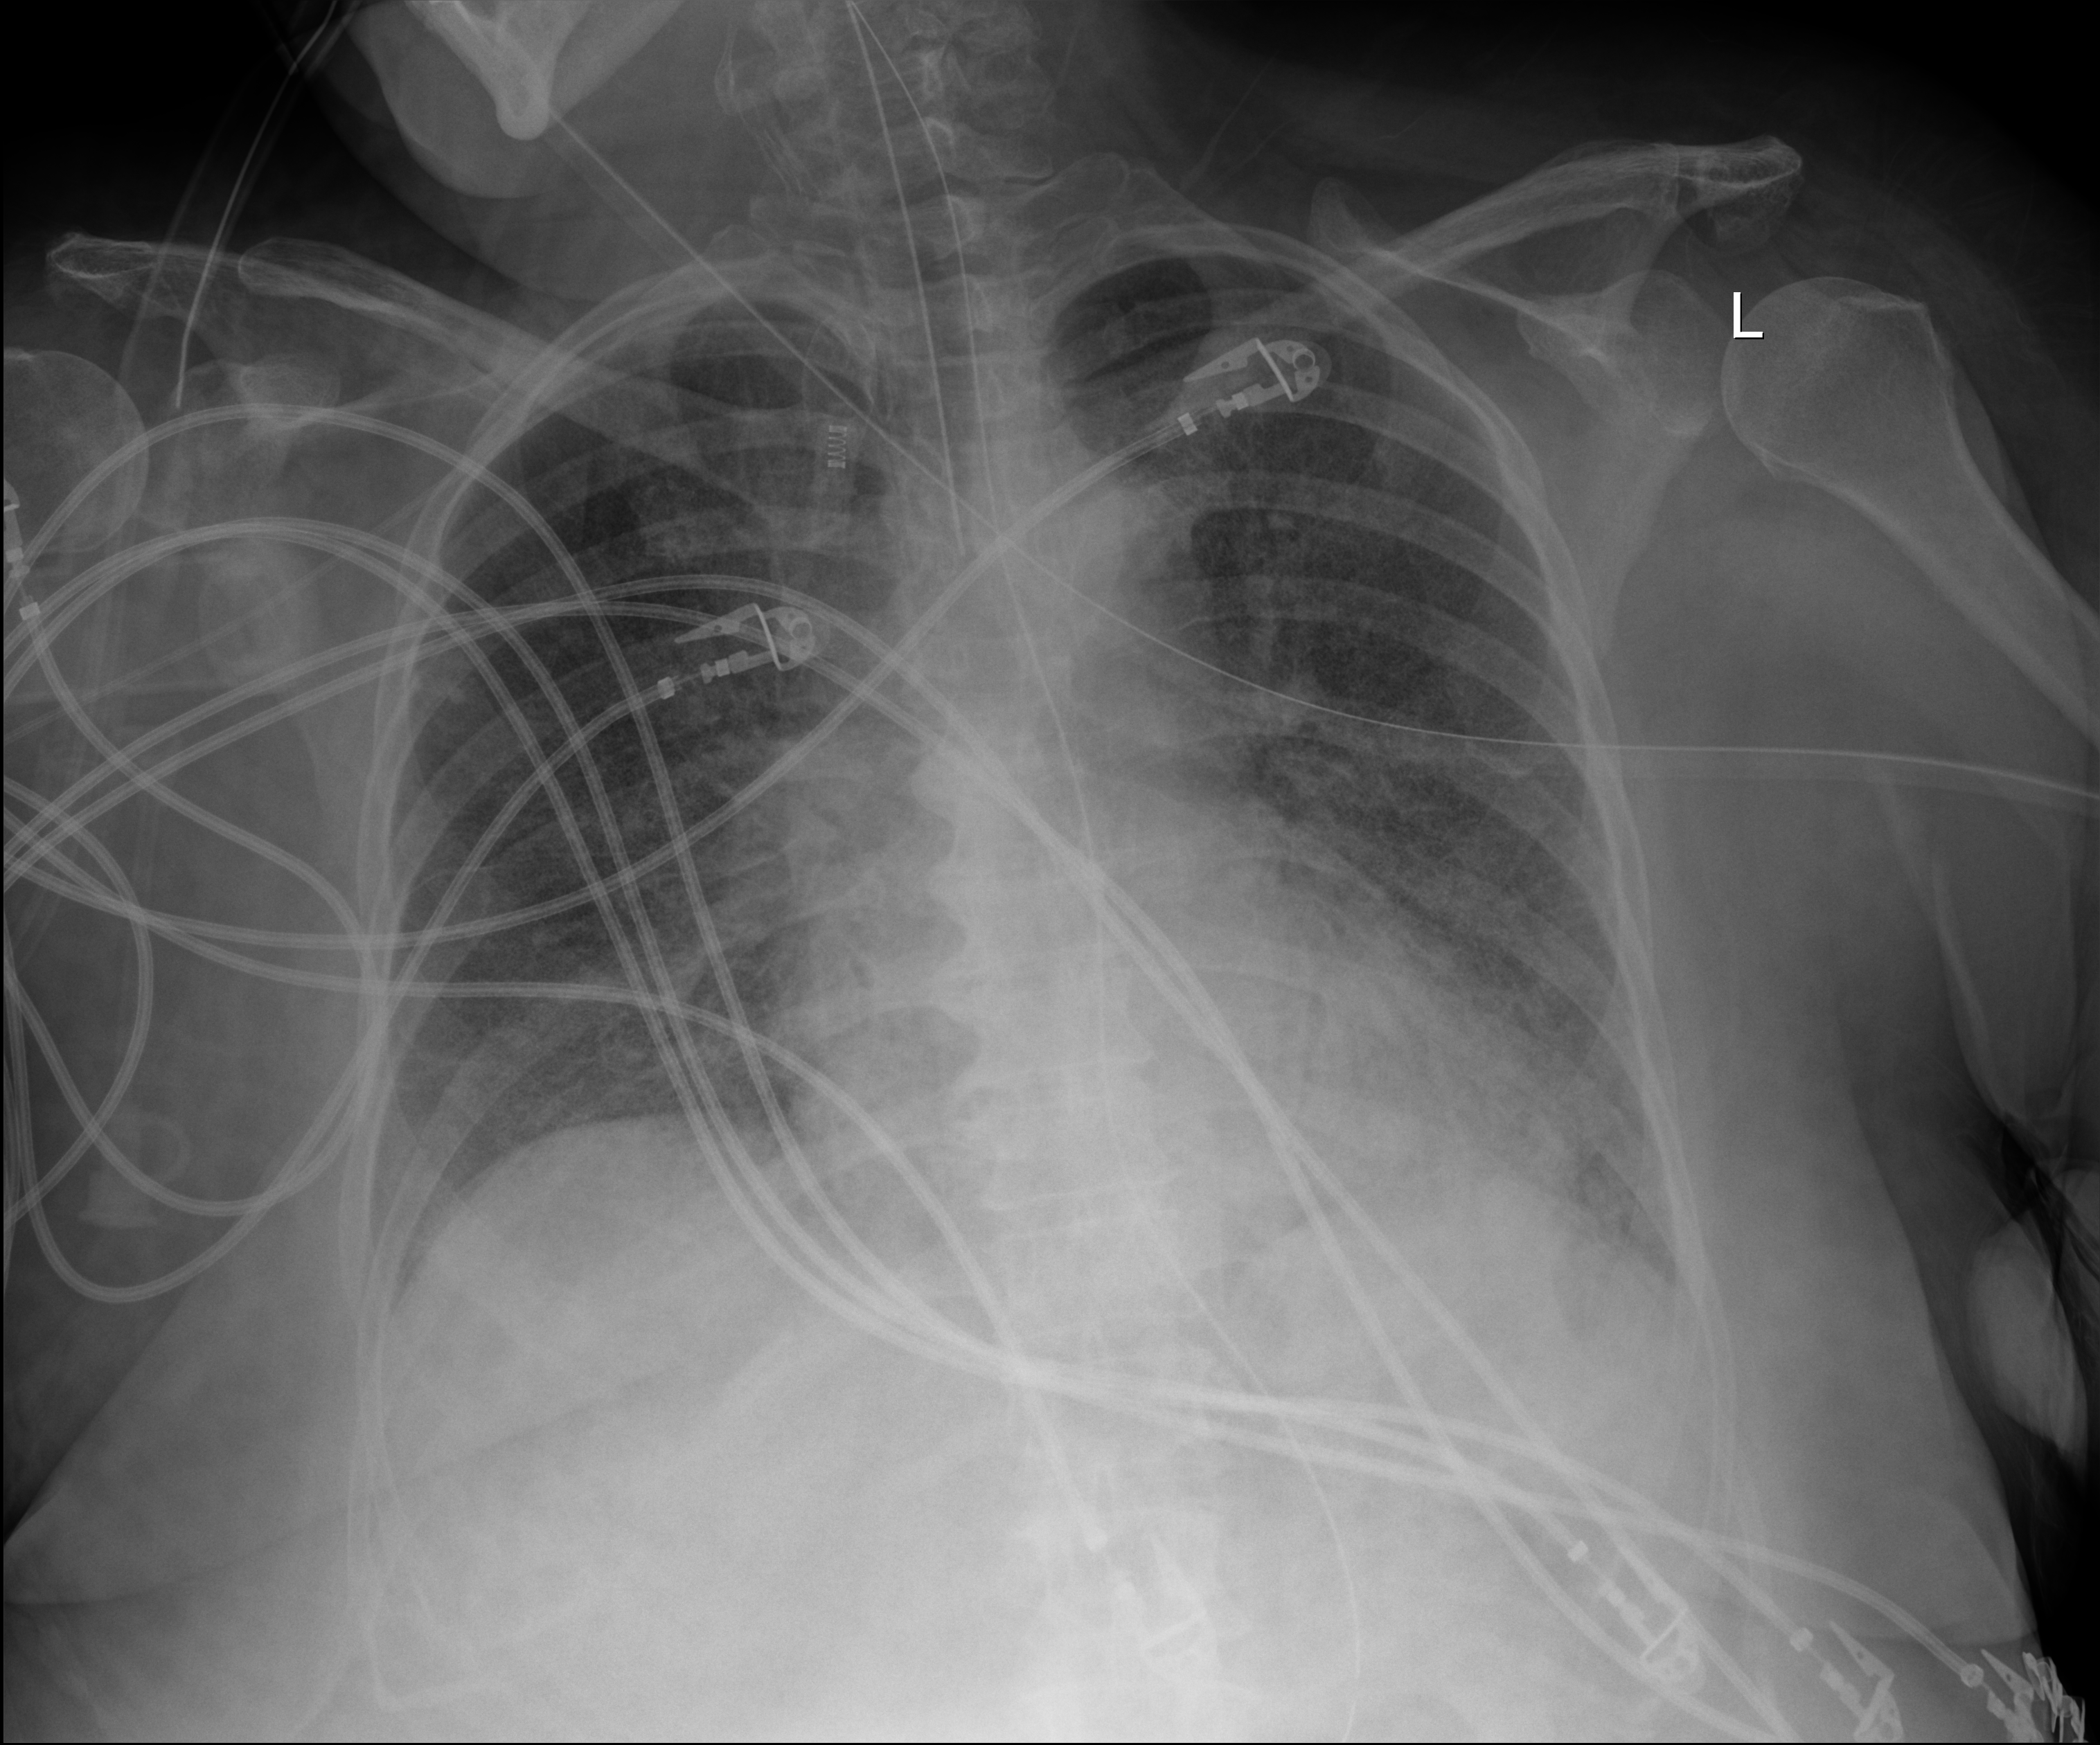
Chest X-ray; anteroposterior (AP) projection. Patient hospitalised with COVID-19; female, aged 60–74 years.
Admission-level facts for this patient (not findings on this image; timing relative to this image not recorded):
- mechanically ventilated during this hospital stay: yes